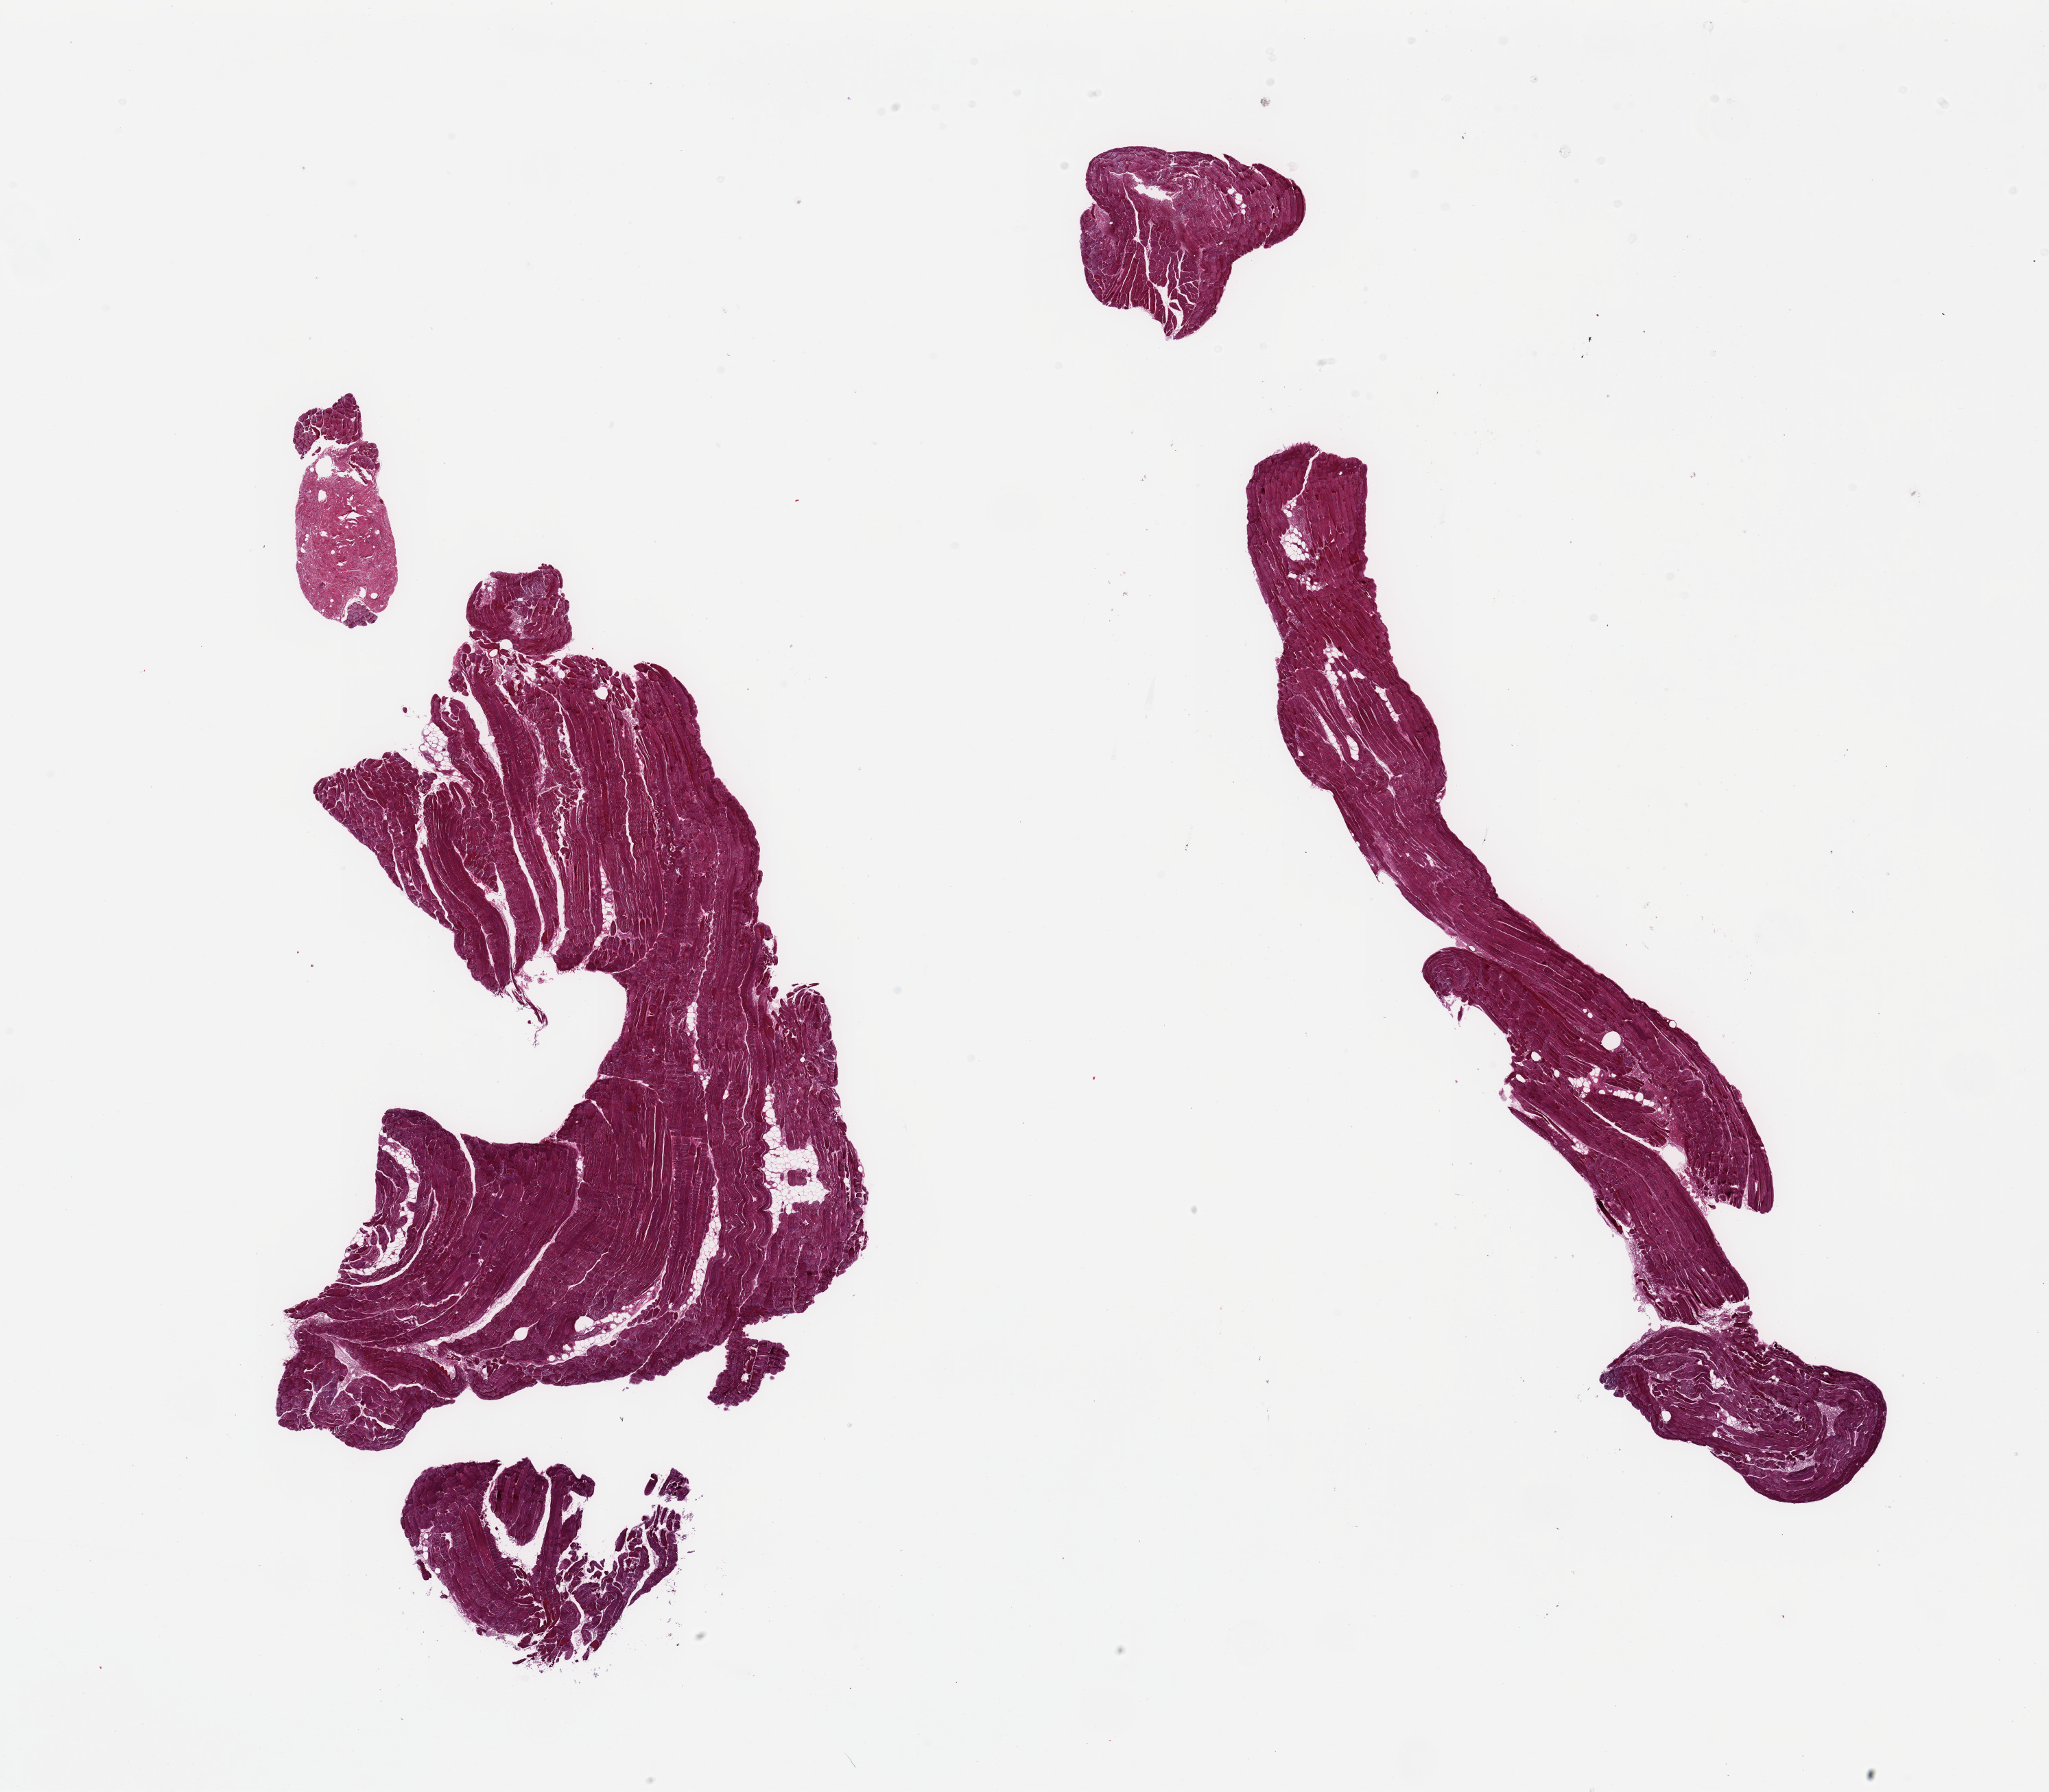
Digitized haematoxylin and eosin-stained section — a low-resolution overview of the entire scanned area, about 23.6 x 20.7 mm (acquisition: 20x scan). PAXgene-fixed paraffin-embedded (PFPE) section. Section of skeletal muscle (target tissue). Donor tissue sample. Female donor.
Review note (as recorded): 2 pieces (fragmented); some atrophy.